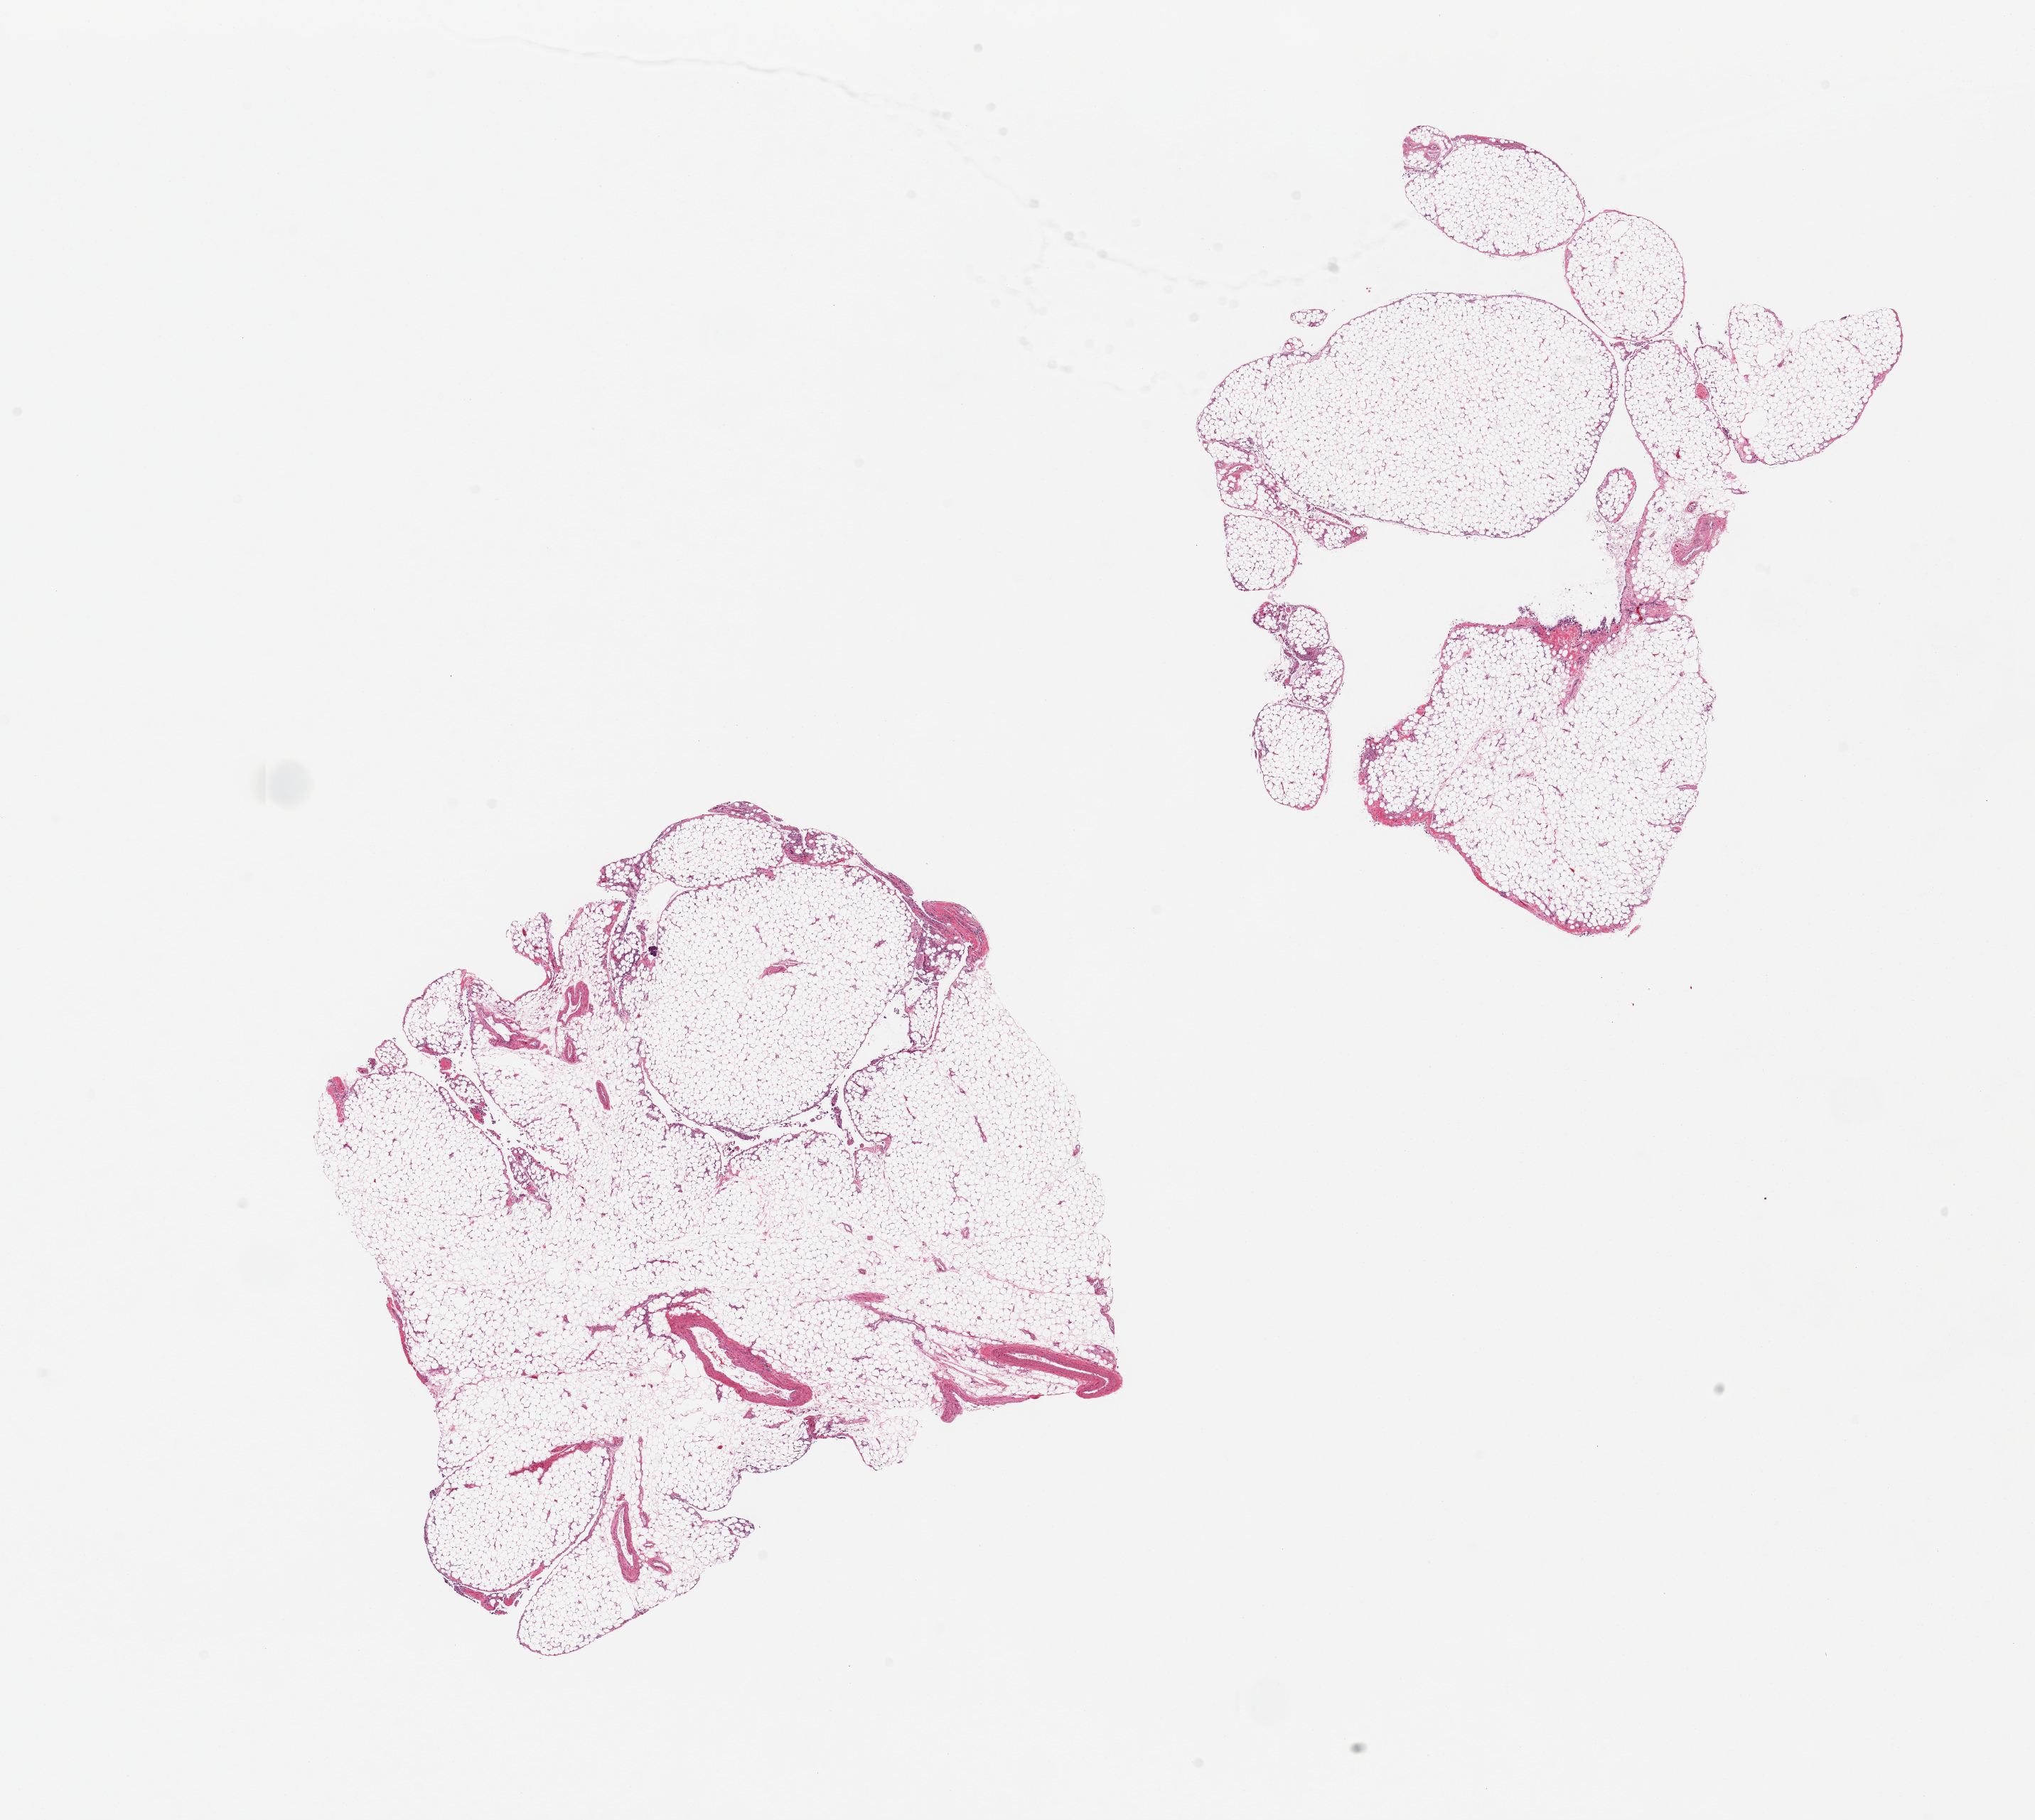
Whole-slide image, haematoxylin and eosin stain — shown as a low-resolution overview of the whole scanned area (about 22.6 x 20.3 mm, slide scanned at 20x), PAXgene-fixed, paraffin-embedded tissue, sampled site (target tissue): omentum, tissue donor sample. Donor: male.
Reviewer comment on this tissue sample: 2 pieces.